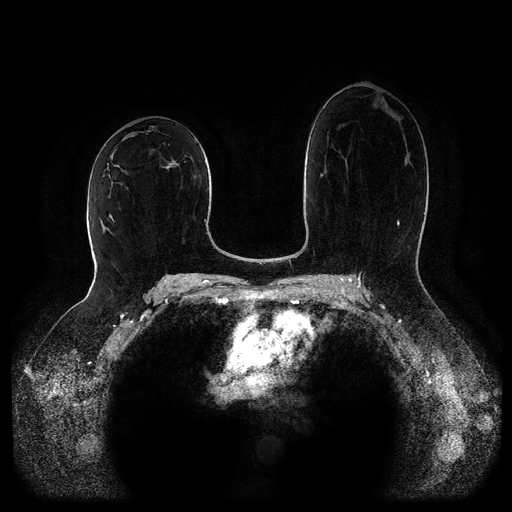
Breast MRI (dynamic contrast-enhanced, multi-phase), one axial slice. Dynamic contrast-enhanced series, time point 2 of 5 at this slice position (early post-contrast). 1.5 T. TE 2.6 ms, TR 5.2 ms. 512 × 512 image matrix, field of view 380 × 380 mm. Patient: female, 52 years.
Outlined on this slice (semi-automatically segmented with operator editing):
- breast lesion (labelled 'tumour' in the annotation; benign lesions carry a separate 'benign' label): bounding box [x1, y1, x2, y2] px = [159, 157, 186, 170]